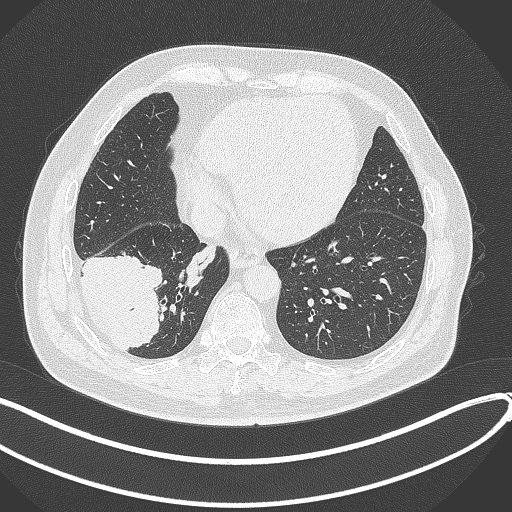
Chest CT, one axial slice; position 108 of 360 along the scan axis; reconstruction kernel B70f; 120 kVp; lung window (W 1500 / L -600 HU); 1 mm slice thickness; 512 × 512 image matrix, field of view 400 × 400 mm. Male patient, age 59 years.
Outlined on this slice (rectangle marked by the reading radiologist):
- lung tumour (recorded histology: adenocarcinoma): bounding box [x1, y1, x2, y2] px = [77, 243, 166, 353]